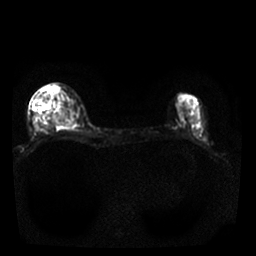
Breast MRI, one axial slice; position 9 of 25 along the scan axis; diffusion-weighted series; image 2 of 4 stored at this slice position (different b-values; order by instance number); 1.5 T; 4 mm slice thickness; 256 × 256 image matrix, field of view 310 × 310 mm. Female patient.
Structures marked on this image (outlined manually by an expert reader):
- tumour on diffusion-weighted imaging: box from (x=52, y=114) to (x=59, y=124) px